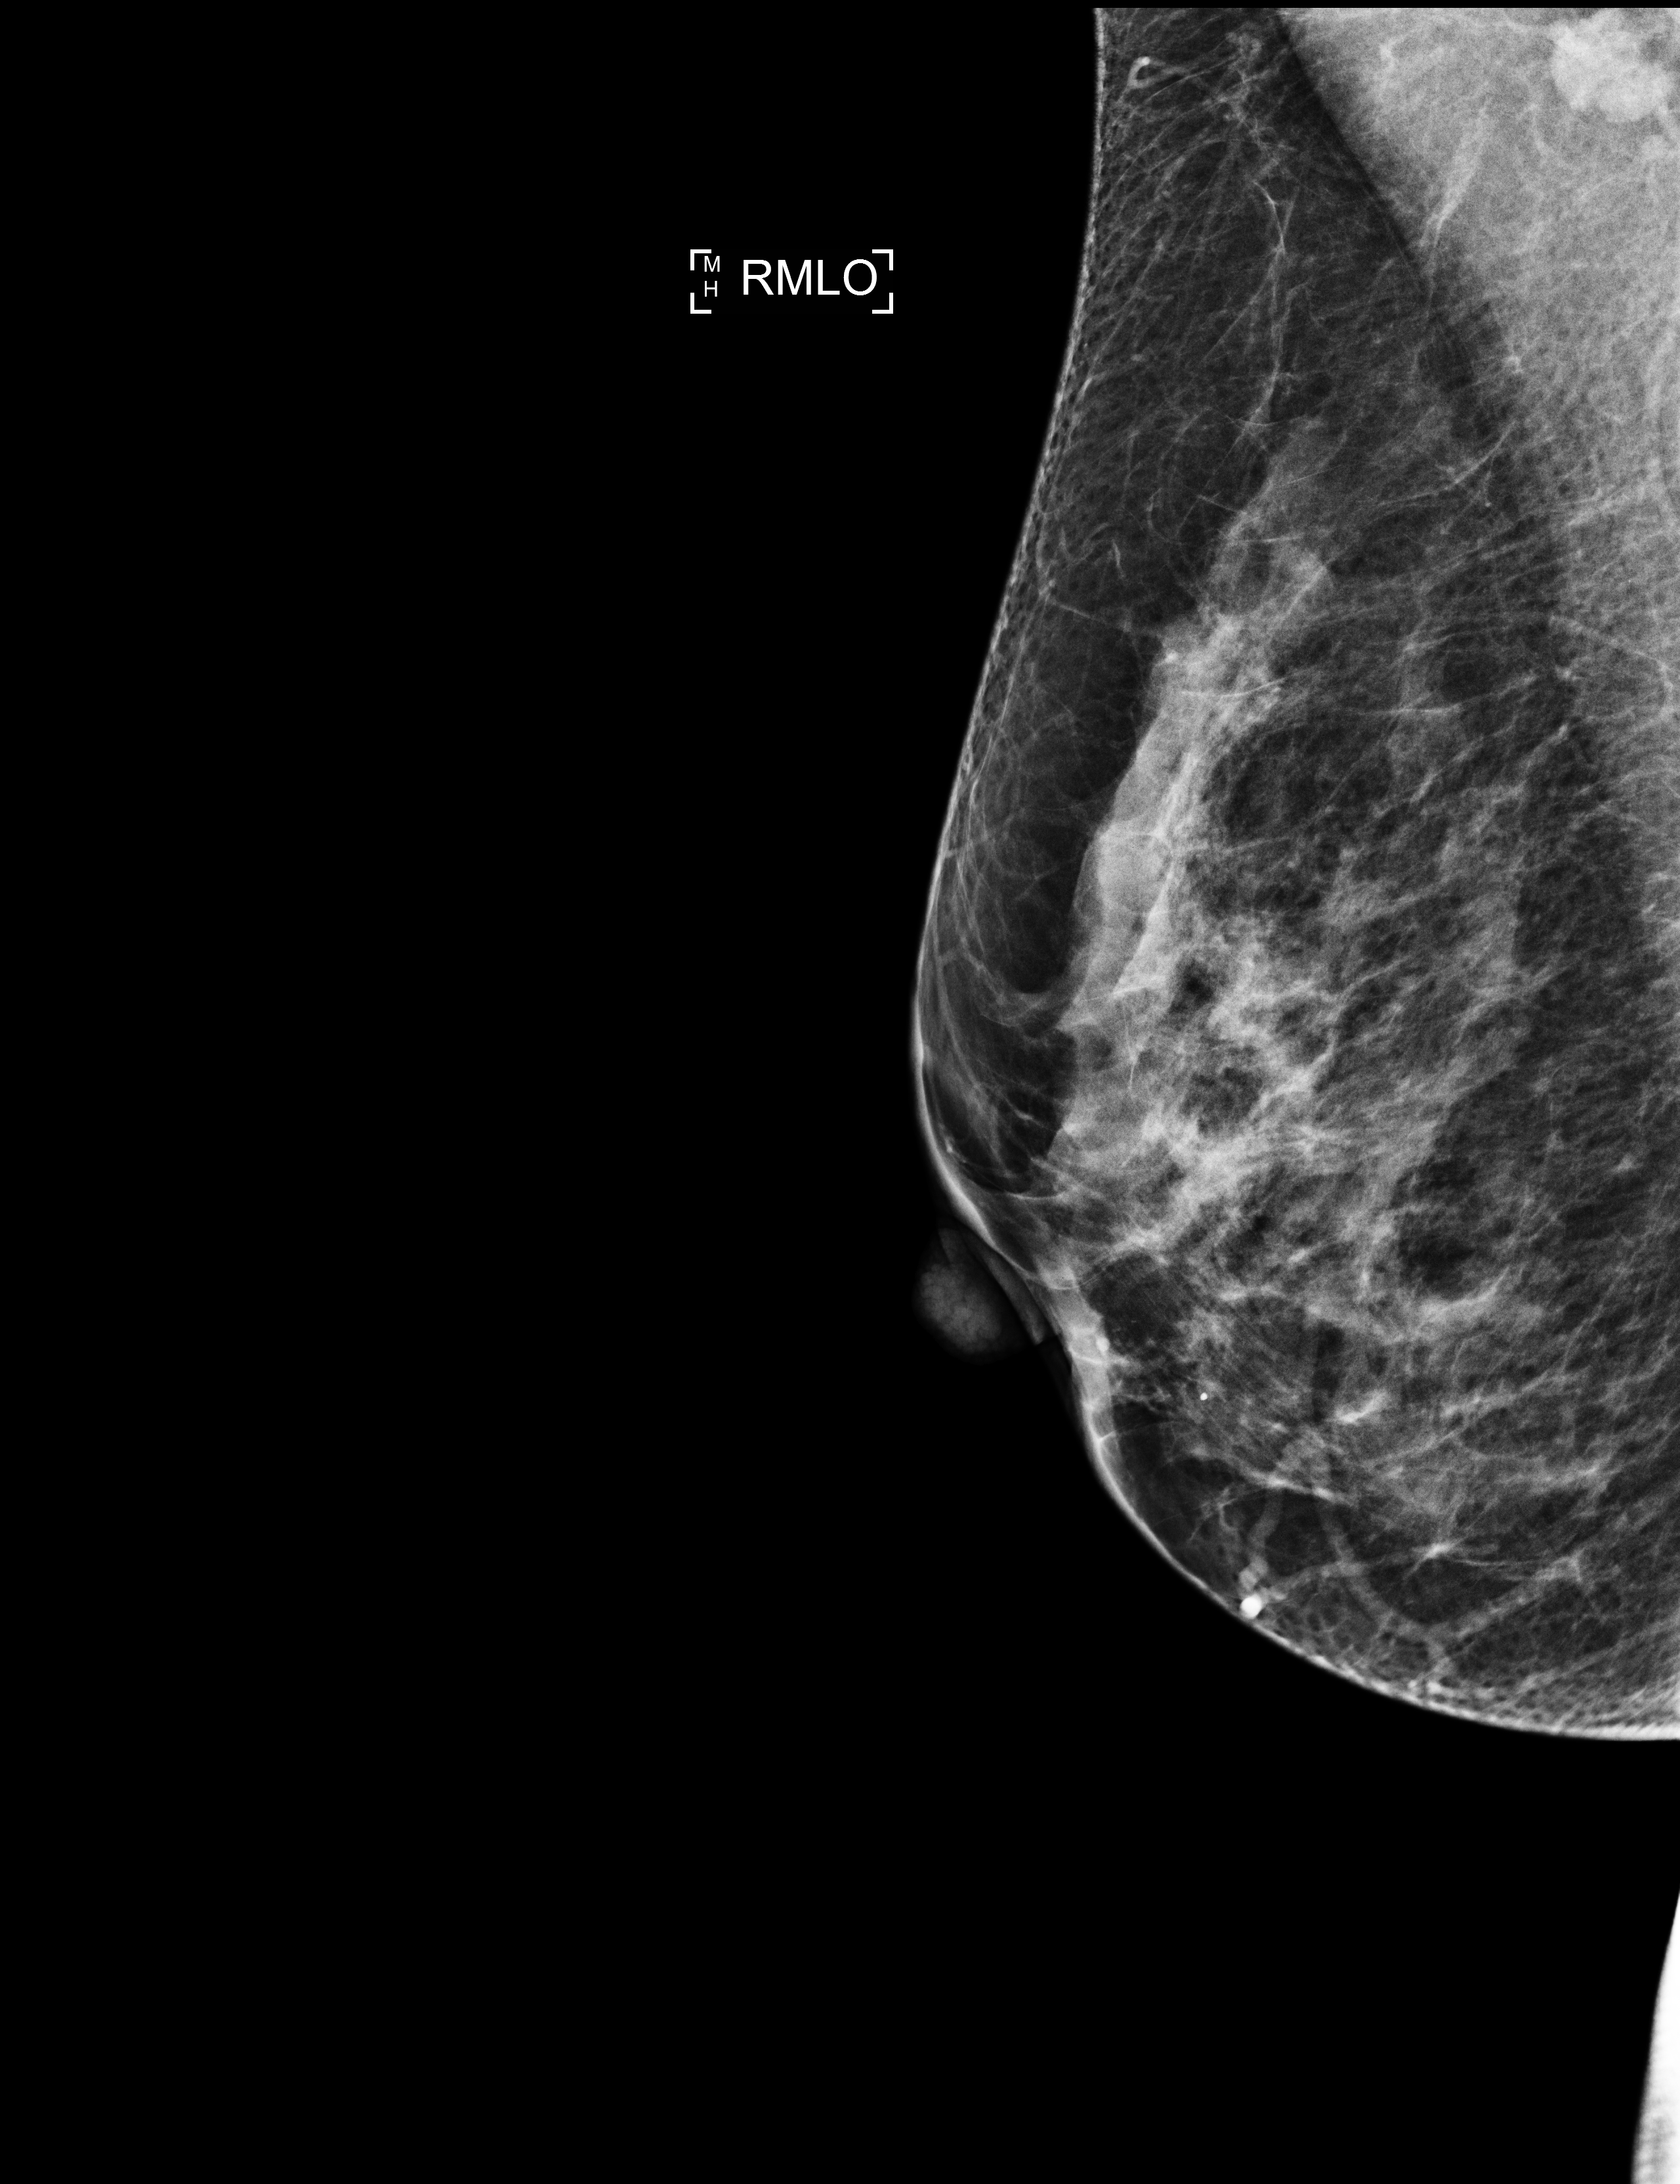
Full-field digital mammogram (FFDM), right breast, mediolateral oblique (MLO) view, screening examination, compressed breast thickness 53 mm. Patient aged 51 years (female).
- breast density at the screening exam (both breasts): heterogeneously dense (BI-RADS density category c)
- final BI-RADS assessment for this screening round (tomosynthesis exam, both breasts): category 1
- recall: no recall after this screen